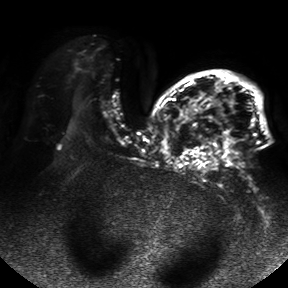
Breast MRI, one axial slice. Position 30 of 50 along the scan axis. Diffusion-weighted series; image 2 of 4 stored at this slice position (different b-values; order by instance number). 1.5 T. 288 × 288 image matrix. Female patient.
Structures marked on this image (manually delineated by an expert):
- tumour on diffusion-weighted imaging: box from (x=224, y=138) to (x=230, y=154) px